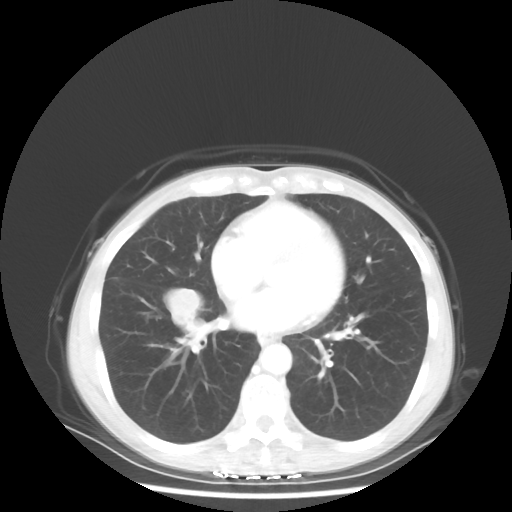
Chest CT, one axial slice. Position 22 of 56 along the scan axis. Reconstruction kernel STANDARD. 80 kVp. Lung window (W 1500 / L -600 HU). 5 mm slice thickness. 512 × 512 image matrix. Patient: female, 57 years. From the clinical record (not read from this slice): clinical TNM (as recorded): T1c N3 M1a; histopathological grade: G3.
Annotated regions visible in this slice (rectangle marked by the reading radiologist):
- lung tumour (recorded histology: adenocarcinoma): bounding box <166,286,203,327> (left, top, right, bottom; pixels)